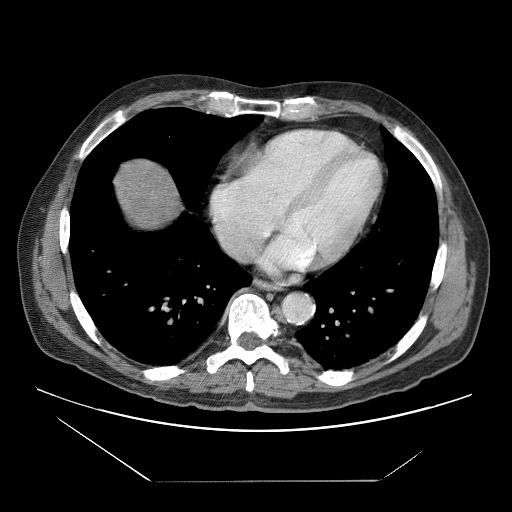
Contrast-enhanced abdominal CT (liver protocol), one axial slice. Slice 75 of 83 in the series (ordered by position). Reconstruction kernel STANDARD. Soft-tissue window (W 400 / L 40 HU). 2.5 mm slice thickness. 512 × 512 image matrix, field of view 420 × 420 mm. From the clinical record (not read from this slice): diagnosis: hepatocellular carcinoma (patient treated with transarterial chemoembolisation; whether this scan precedes or follows treatment is not stated here); TNM stage (as recorded): Stage-IVB; Child-Pugh class: B; tumour nodularity: uninodular.
Structures marked on this image (semi-automatically segmented with operator editing):
- abdominal aorta: bounding box (x1, y1, x2, y2) in pixels: (284, 294, 313, 321)
- liver parenchyma outside the tumour (the mass and vessels are separate outlines, so this box may not span the whole liver): (114, 158, 179, 228)